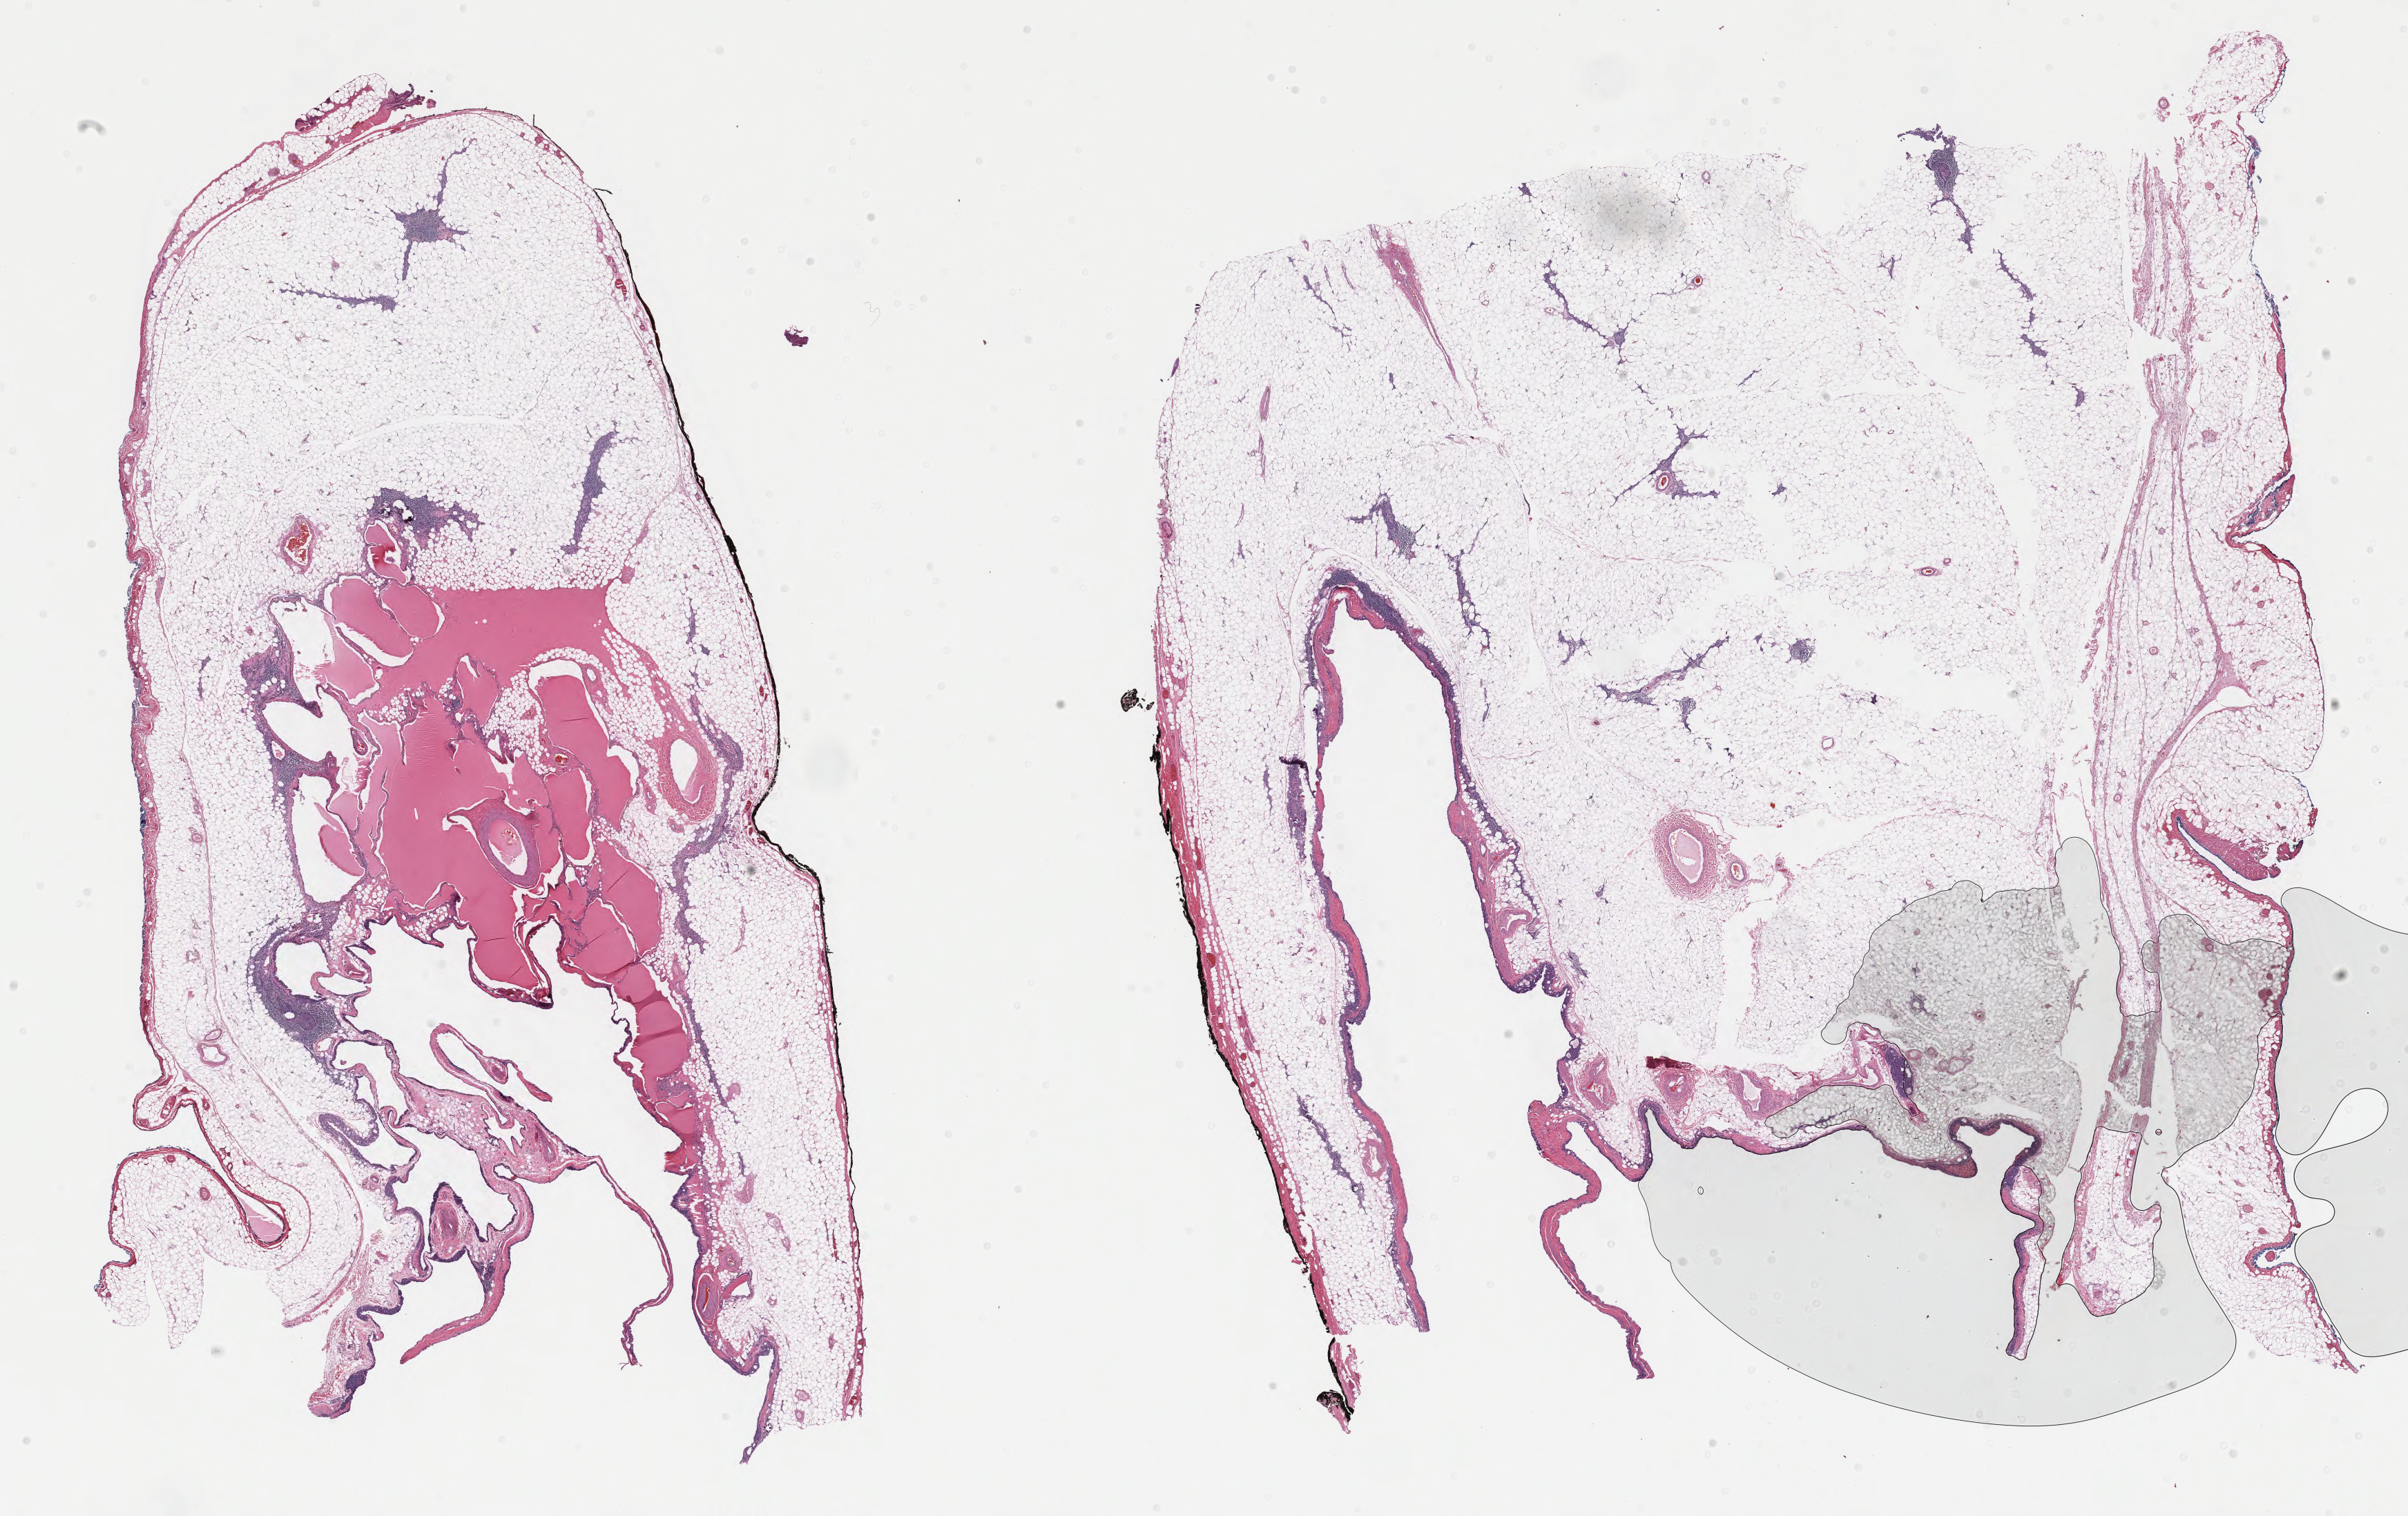
Whole-slide histology image, H&E — whole scanned area (about 27.6 x 17.4 mm, slide scanned at 40x) shown as a low-resolution overview. FFPE section. Thymus, primary tumour sample. Male, age 52 years at initial diagnosis.
Histologic diagnosis: Thymoma, type A, malignant.